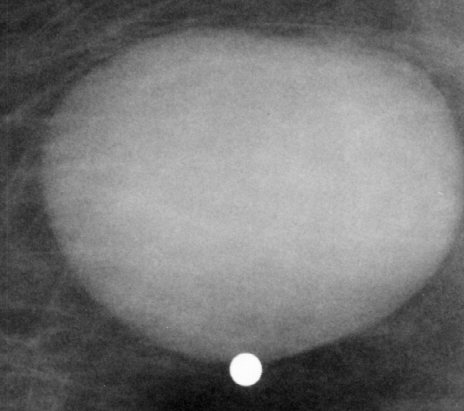
Crop from a digitized film mammogram around one marked abnormality; right breast; MLO view; BI-RADS breast density category 1 (scale 1–4).
- Marked abnormality: mass, shape oval, margins circumscribed; BI-RADS assessment category 4; pathology result (as recorded, not read from the image): benign.